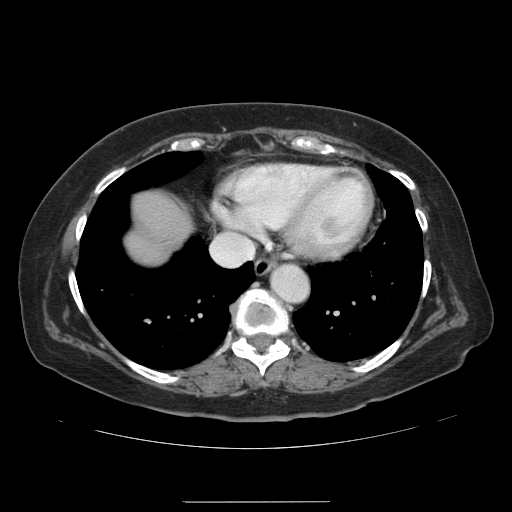
Contrast-enhanced abdominal CT, one axial slice. Intravenous contrast given. Soft-tissue window (W 400 / L 40 HU). 2.5 mm slice thickness. 512 × 512 image matrix, field of view 393 × 393 mm. Female patient, age 74 years. Case-level facts recorded for this patient, not image findings: diagnosis: colorectal cancer liver metastases, imaged before liver resection; multiple liver metastases: yes; largest metastasis: 7 cm; chemotherapy before resection: no.
Structures marked on this image (expert manual segmentation):
- hepatic veins: bounding box <222,233,244,238> (left, top, right, bottom; pixels)
- liver: <129,195,188,259>
- planned liver remnant (the part of the liver to remain after resection): <134,195,165,258>